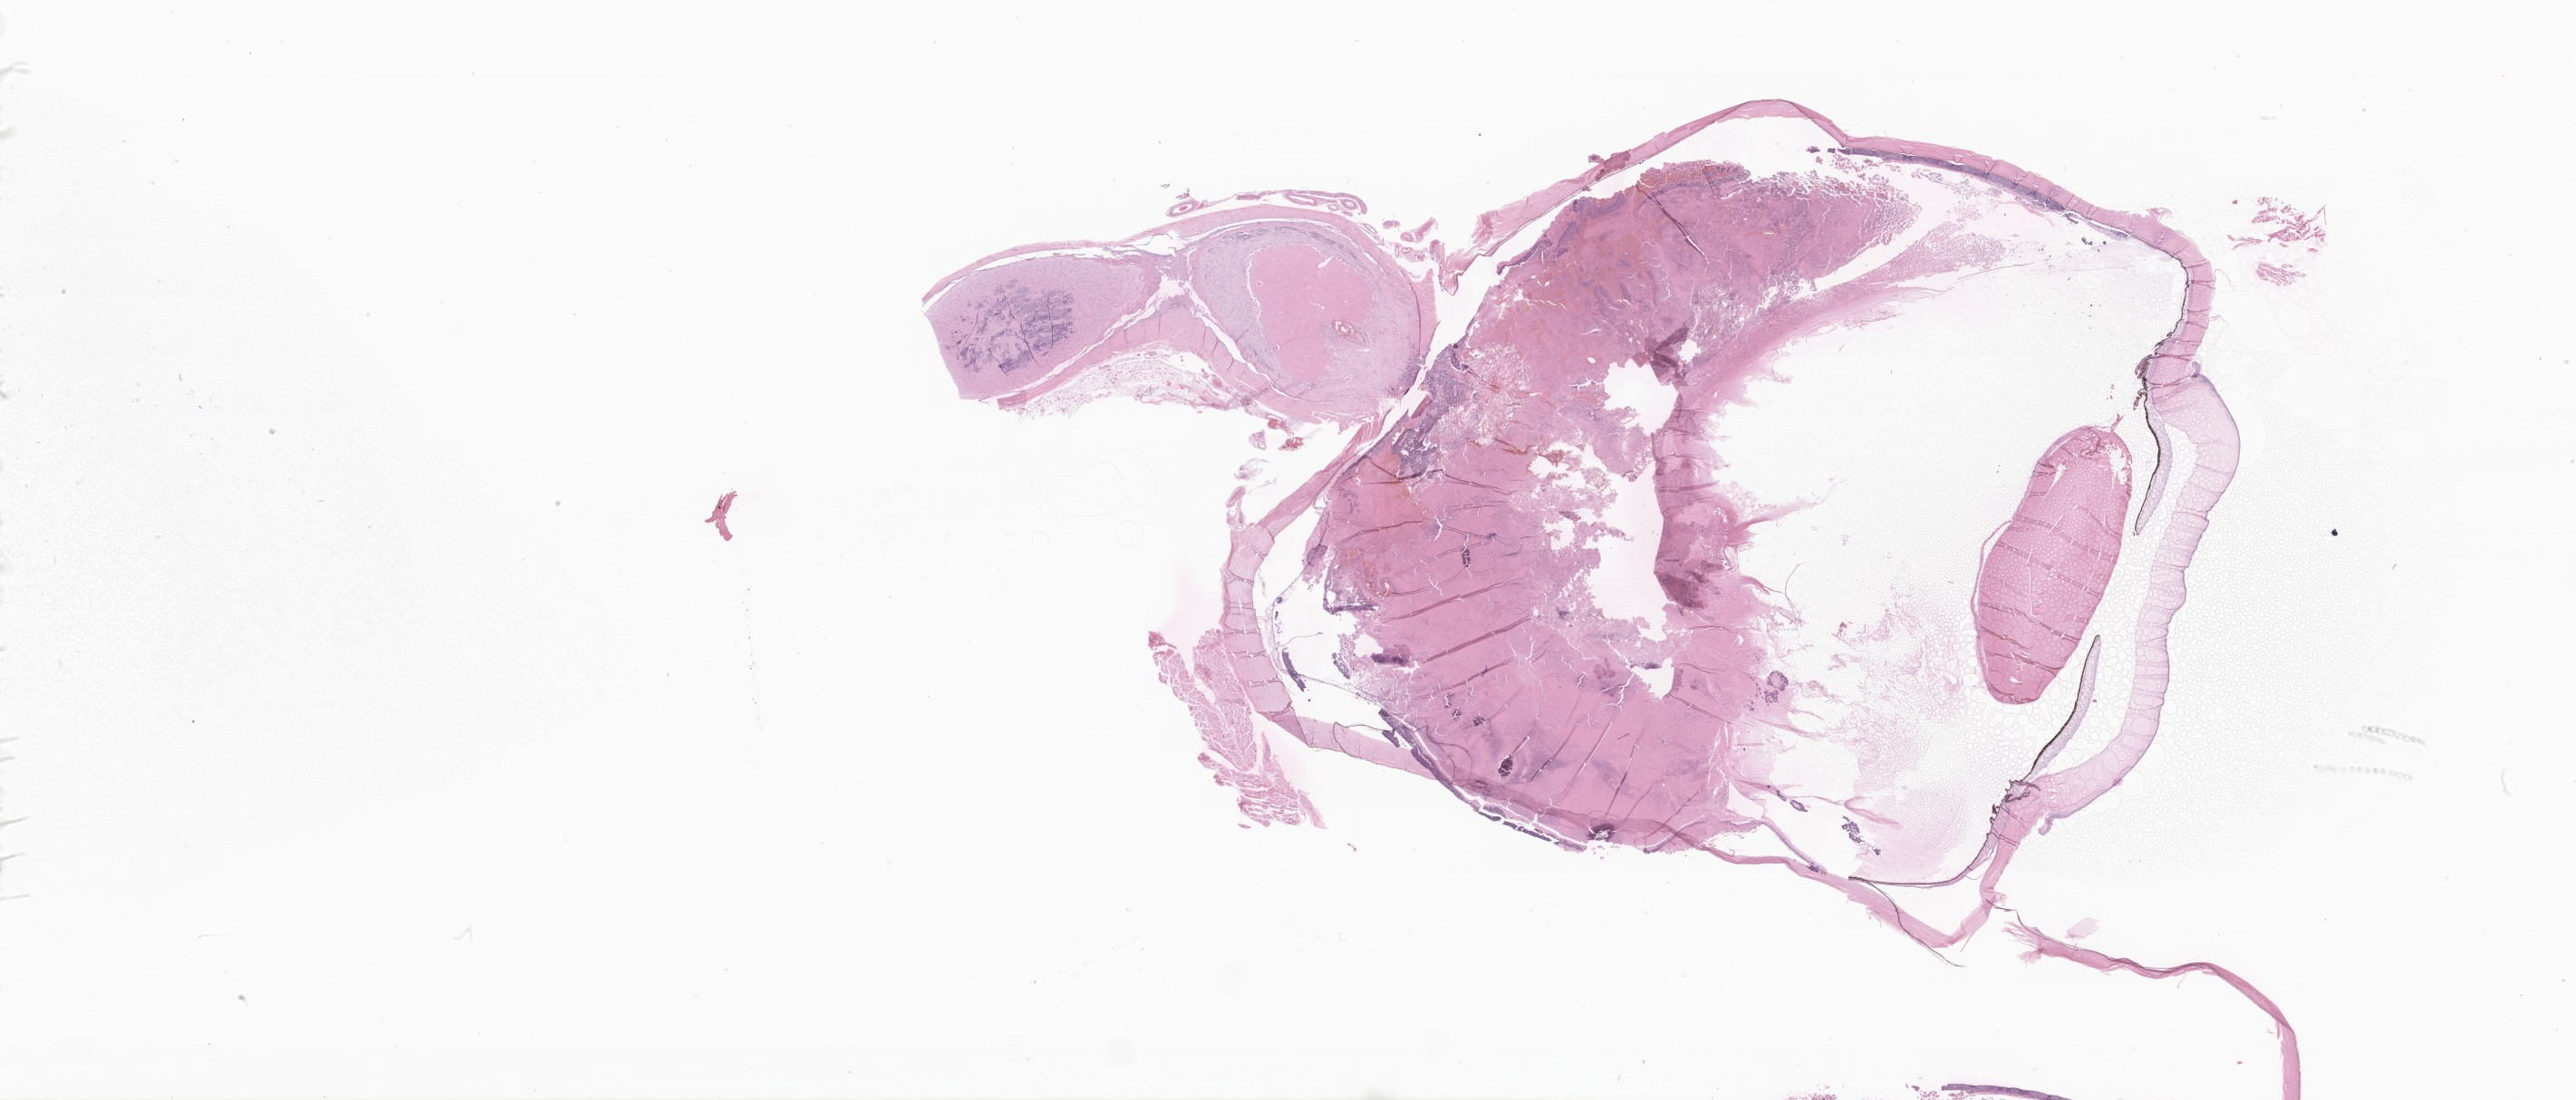
Digitized hematoxylin and eosin (H&E)-stained section of tumor tissue from the eye — a low-resolution overview of the entire scanned area, about 47.9 x 20.5 mm; formalin-fixed paraffin-embedded section. Female patient, age 794 days (about 2.2 years).
Diagnosis: Retinoblastoma, NOS.